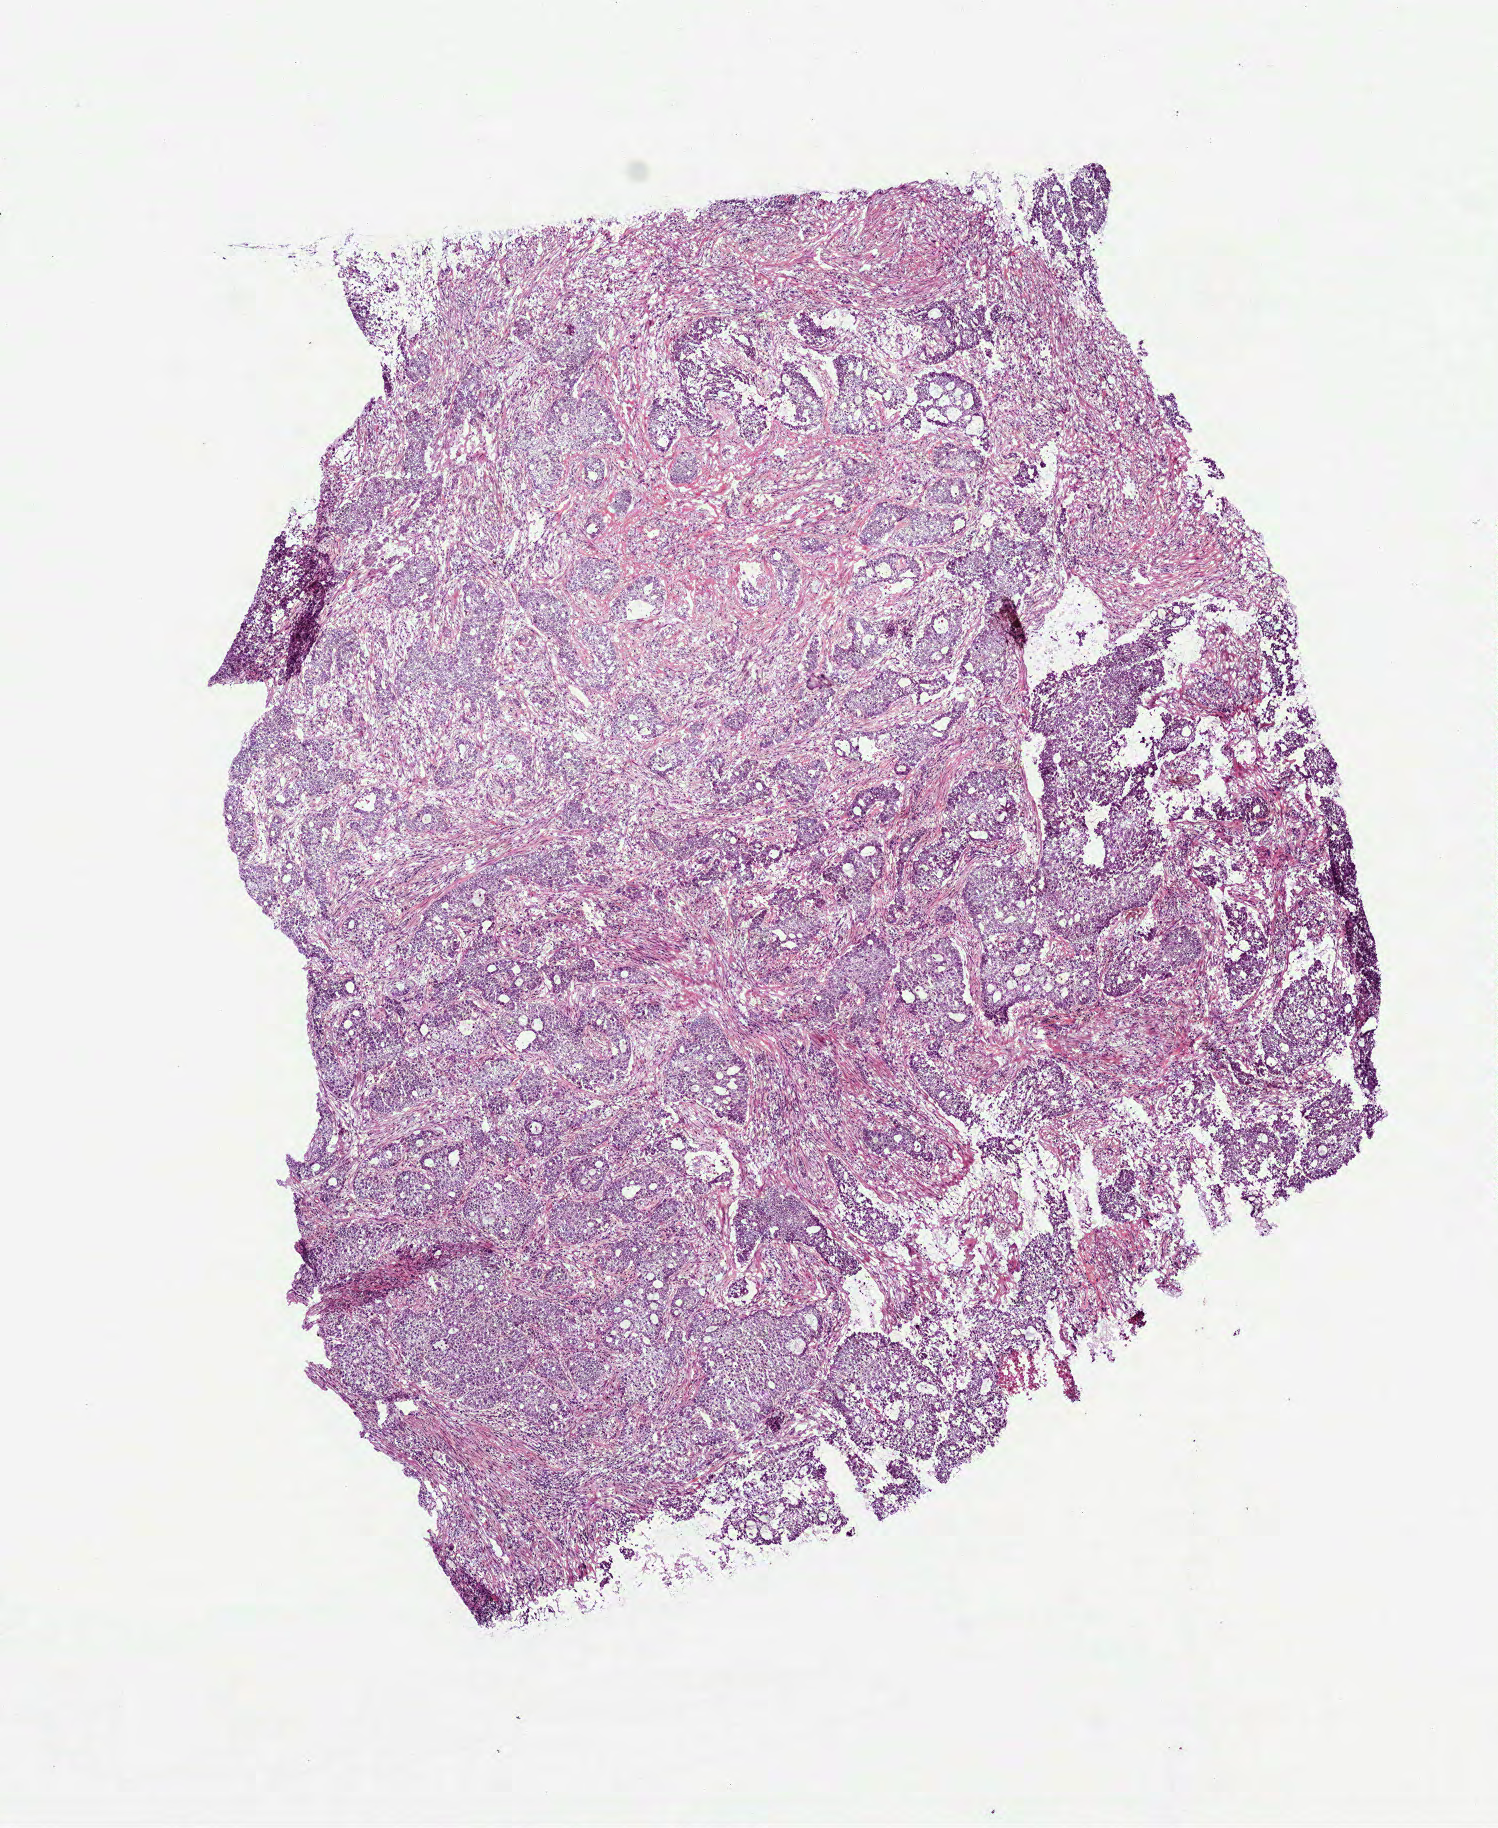
Hematoxylin and eosin (H&E) stained whole-slide image, low-resolution overview of the scanned area, about 6.0 x 7.4 mm; frozen section; sample: primary tumour, lung. Patient sex: male.
Histologic diagnosis: Adenocarcinoma, NOS (lower lobe, lung).